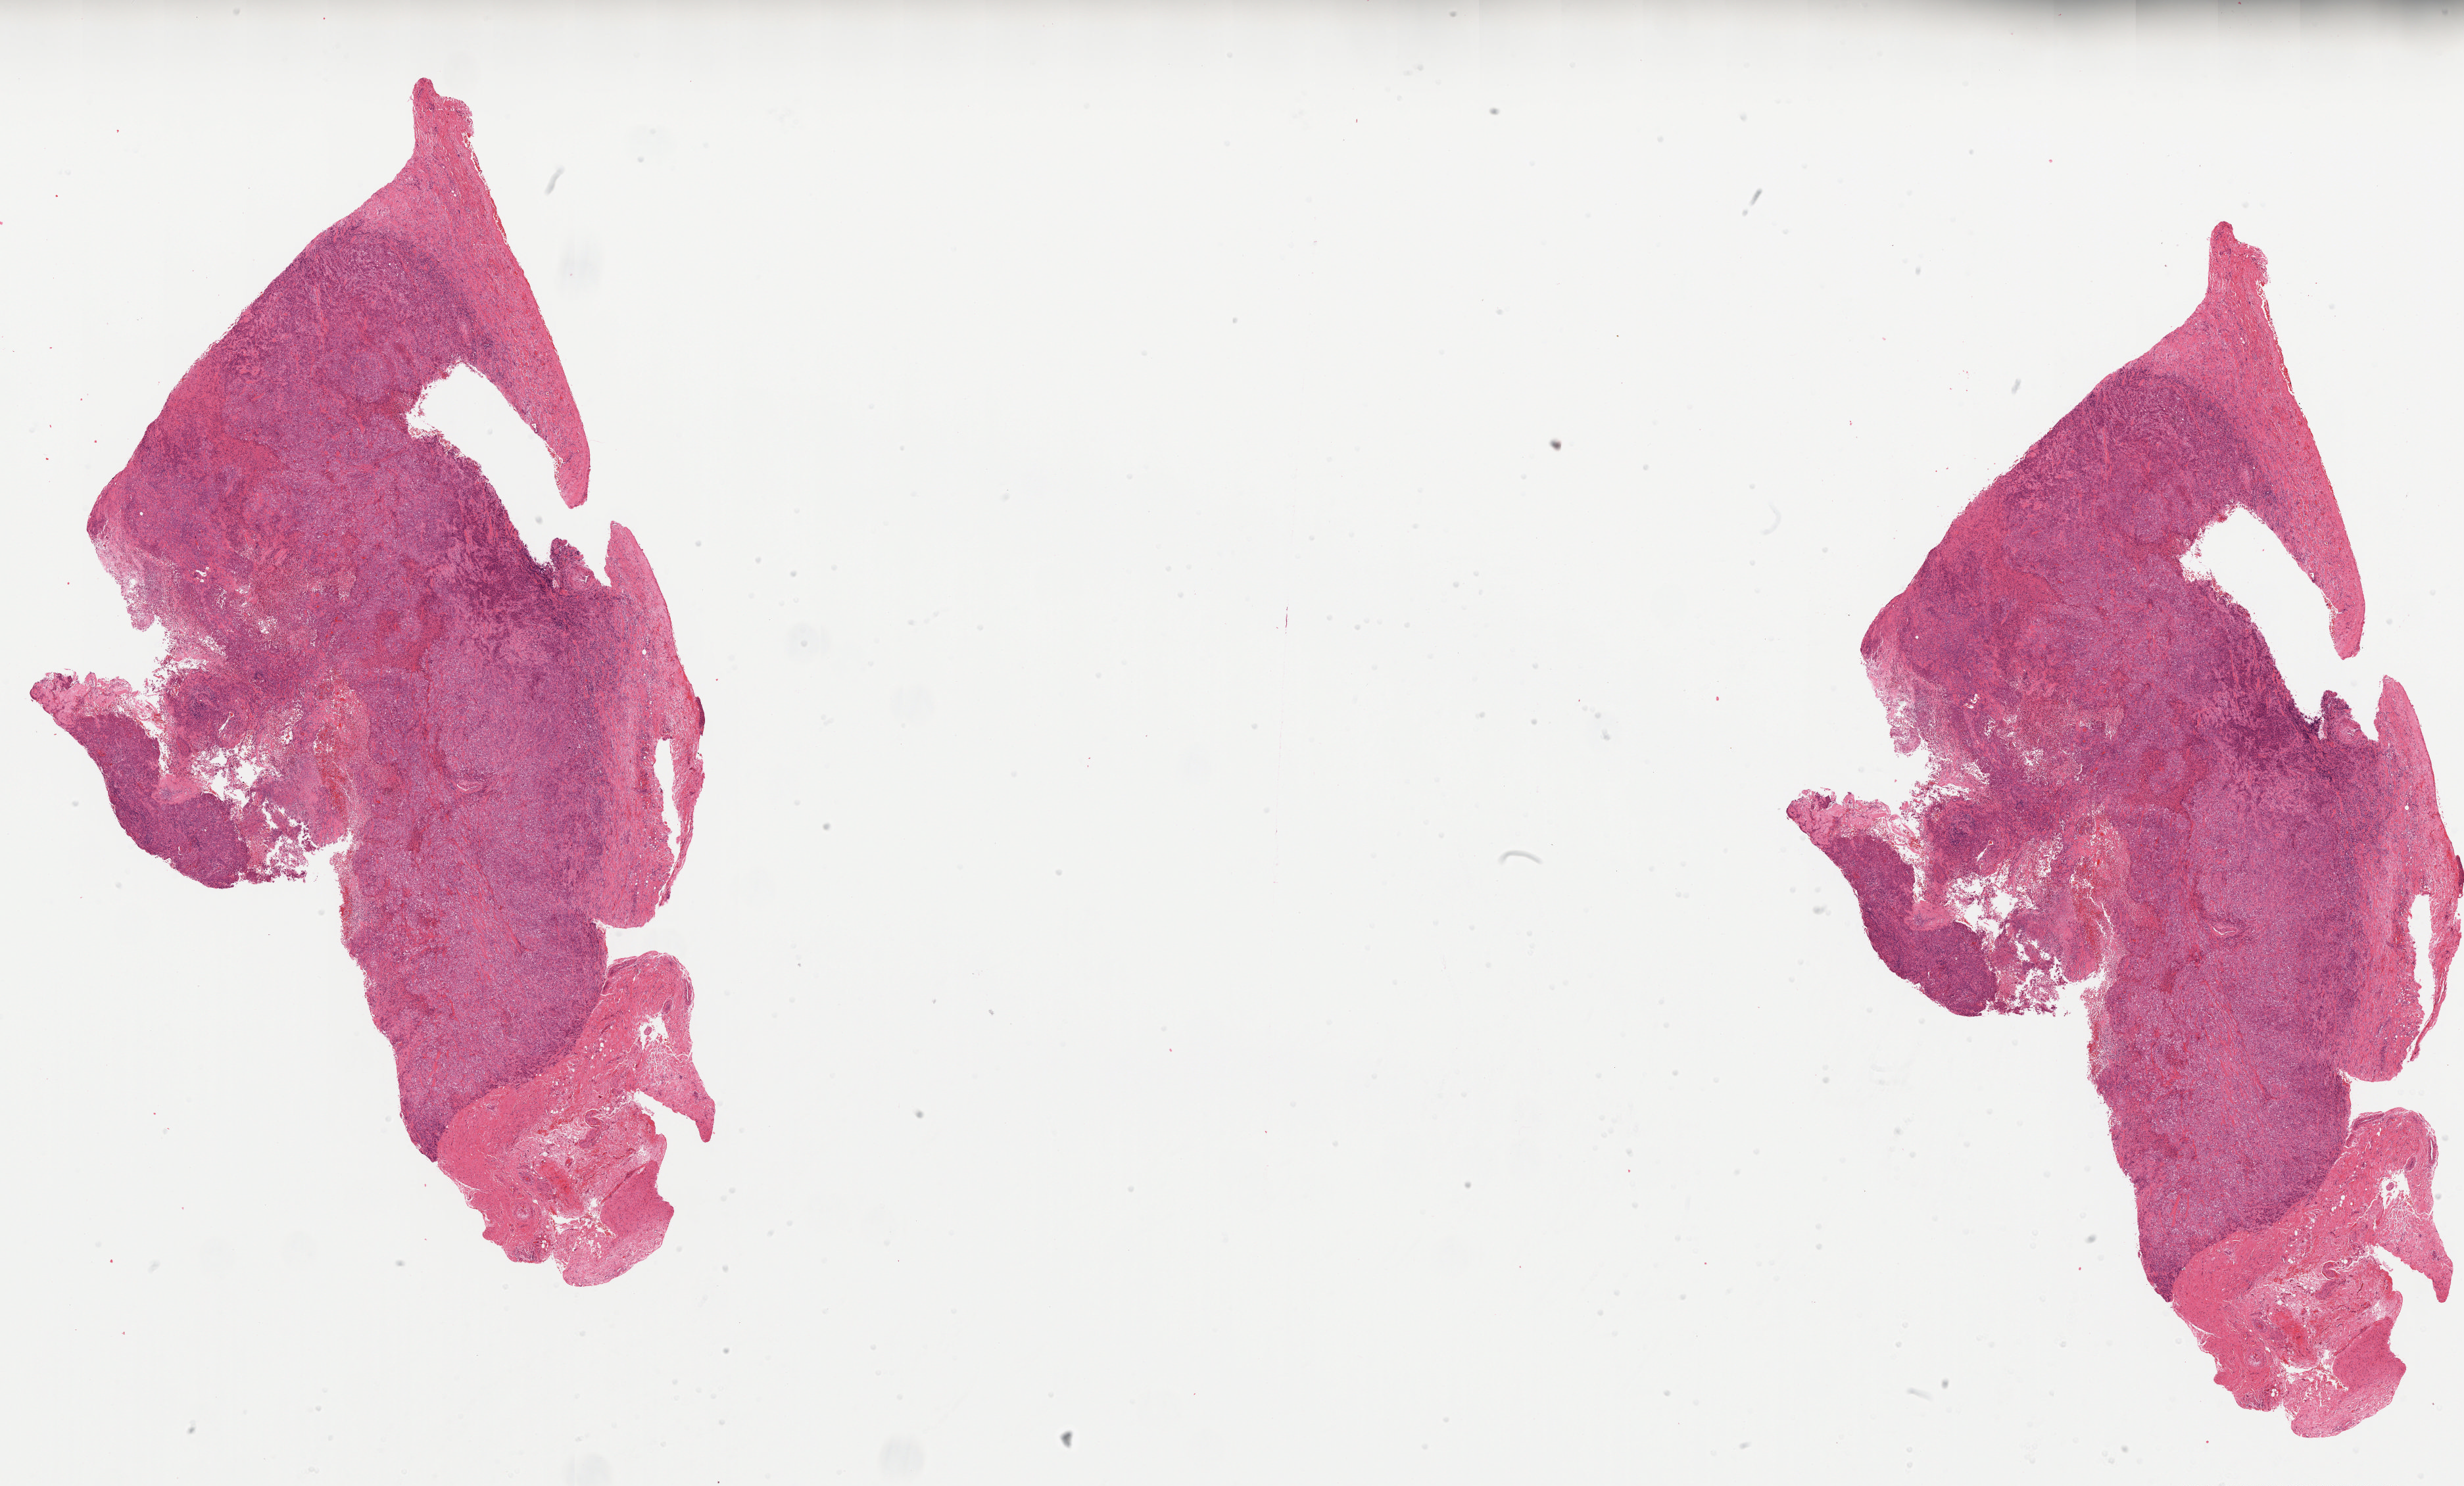
Digitized Hematoxylin and eosin (H&E) stained tissue section (whole slide) — low-resolution overview of the scanned area, about 30.0 x 18.1 mm. FFPE section. Lung, primary tumour sample. Female, age 69 years at initial diagnosis.
Histologic diagnosis: Squamous cell carcinoma, NOS (overlapping lesion of lung).